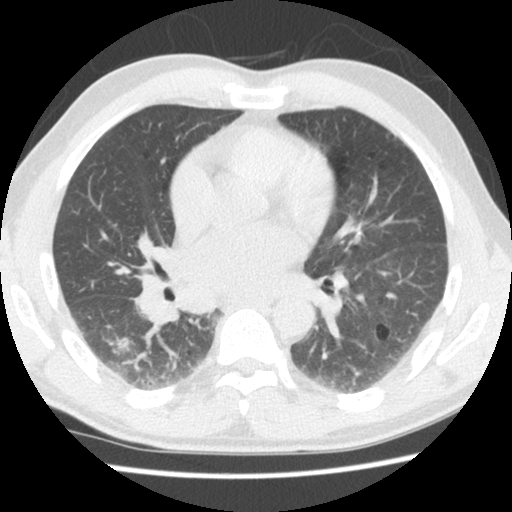
Chest CT (low-dose screening protocol), one axial image; second annual screen; lung window (W 1500 / L -600 HU); 2.5 mm slice thickness; standard (soft-tissue) reconstruction kernel (STANDARD); slice 75 of 133 in the series. Male, age 60 years at enrolment. Former smoker at enrolment.
Expert reader's lesion annotation, bounding box [x1, y1, x2, y2] px = [90, 322, 142, 372]. Reader record for this screening exam (exam-level; its link to the box is not recorded): non-calcified nodule or mass ≥4 mm, right lower lobe, 17 × 15 mm, poorly defined margins, soft tissue attenuation, pre-existing on the prior screen: yes; interval growth: yes. Official screen result: positive, other.